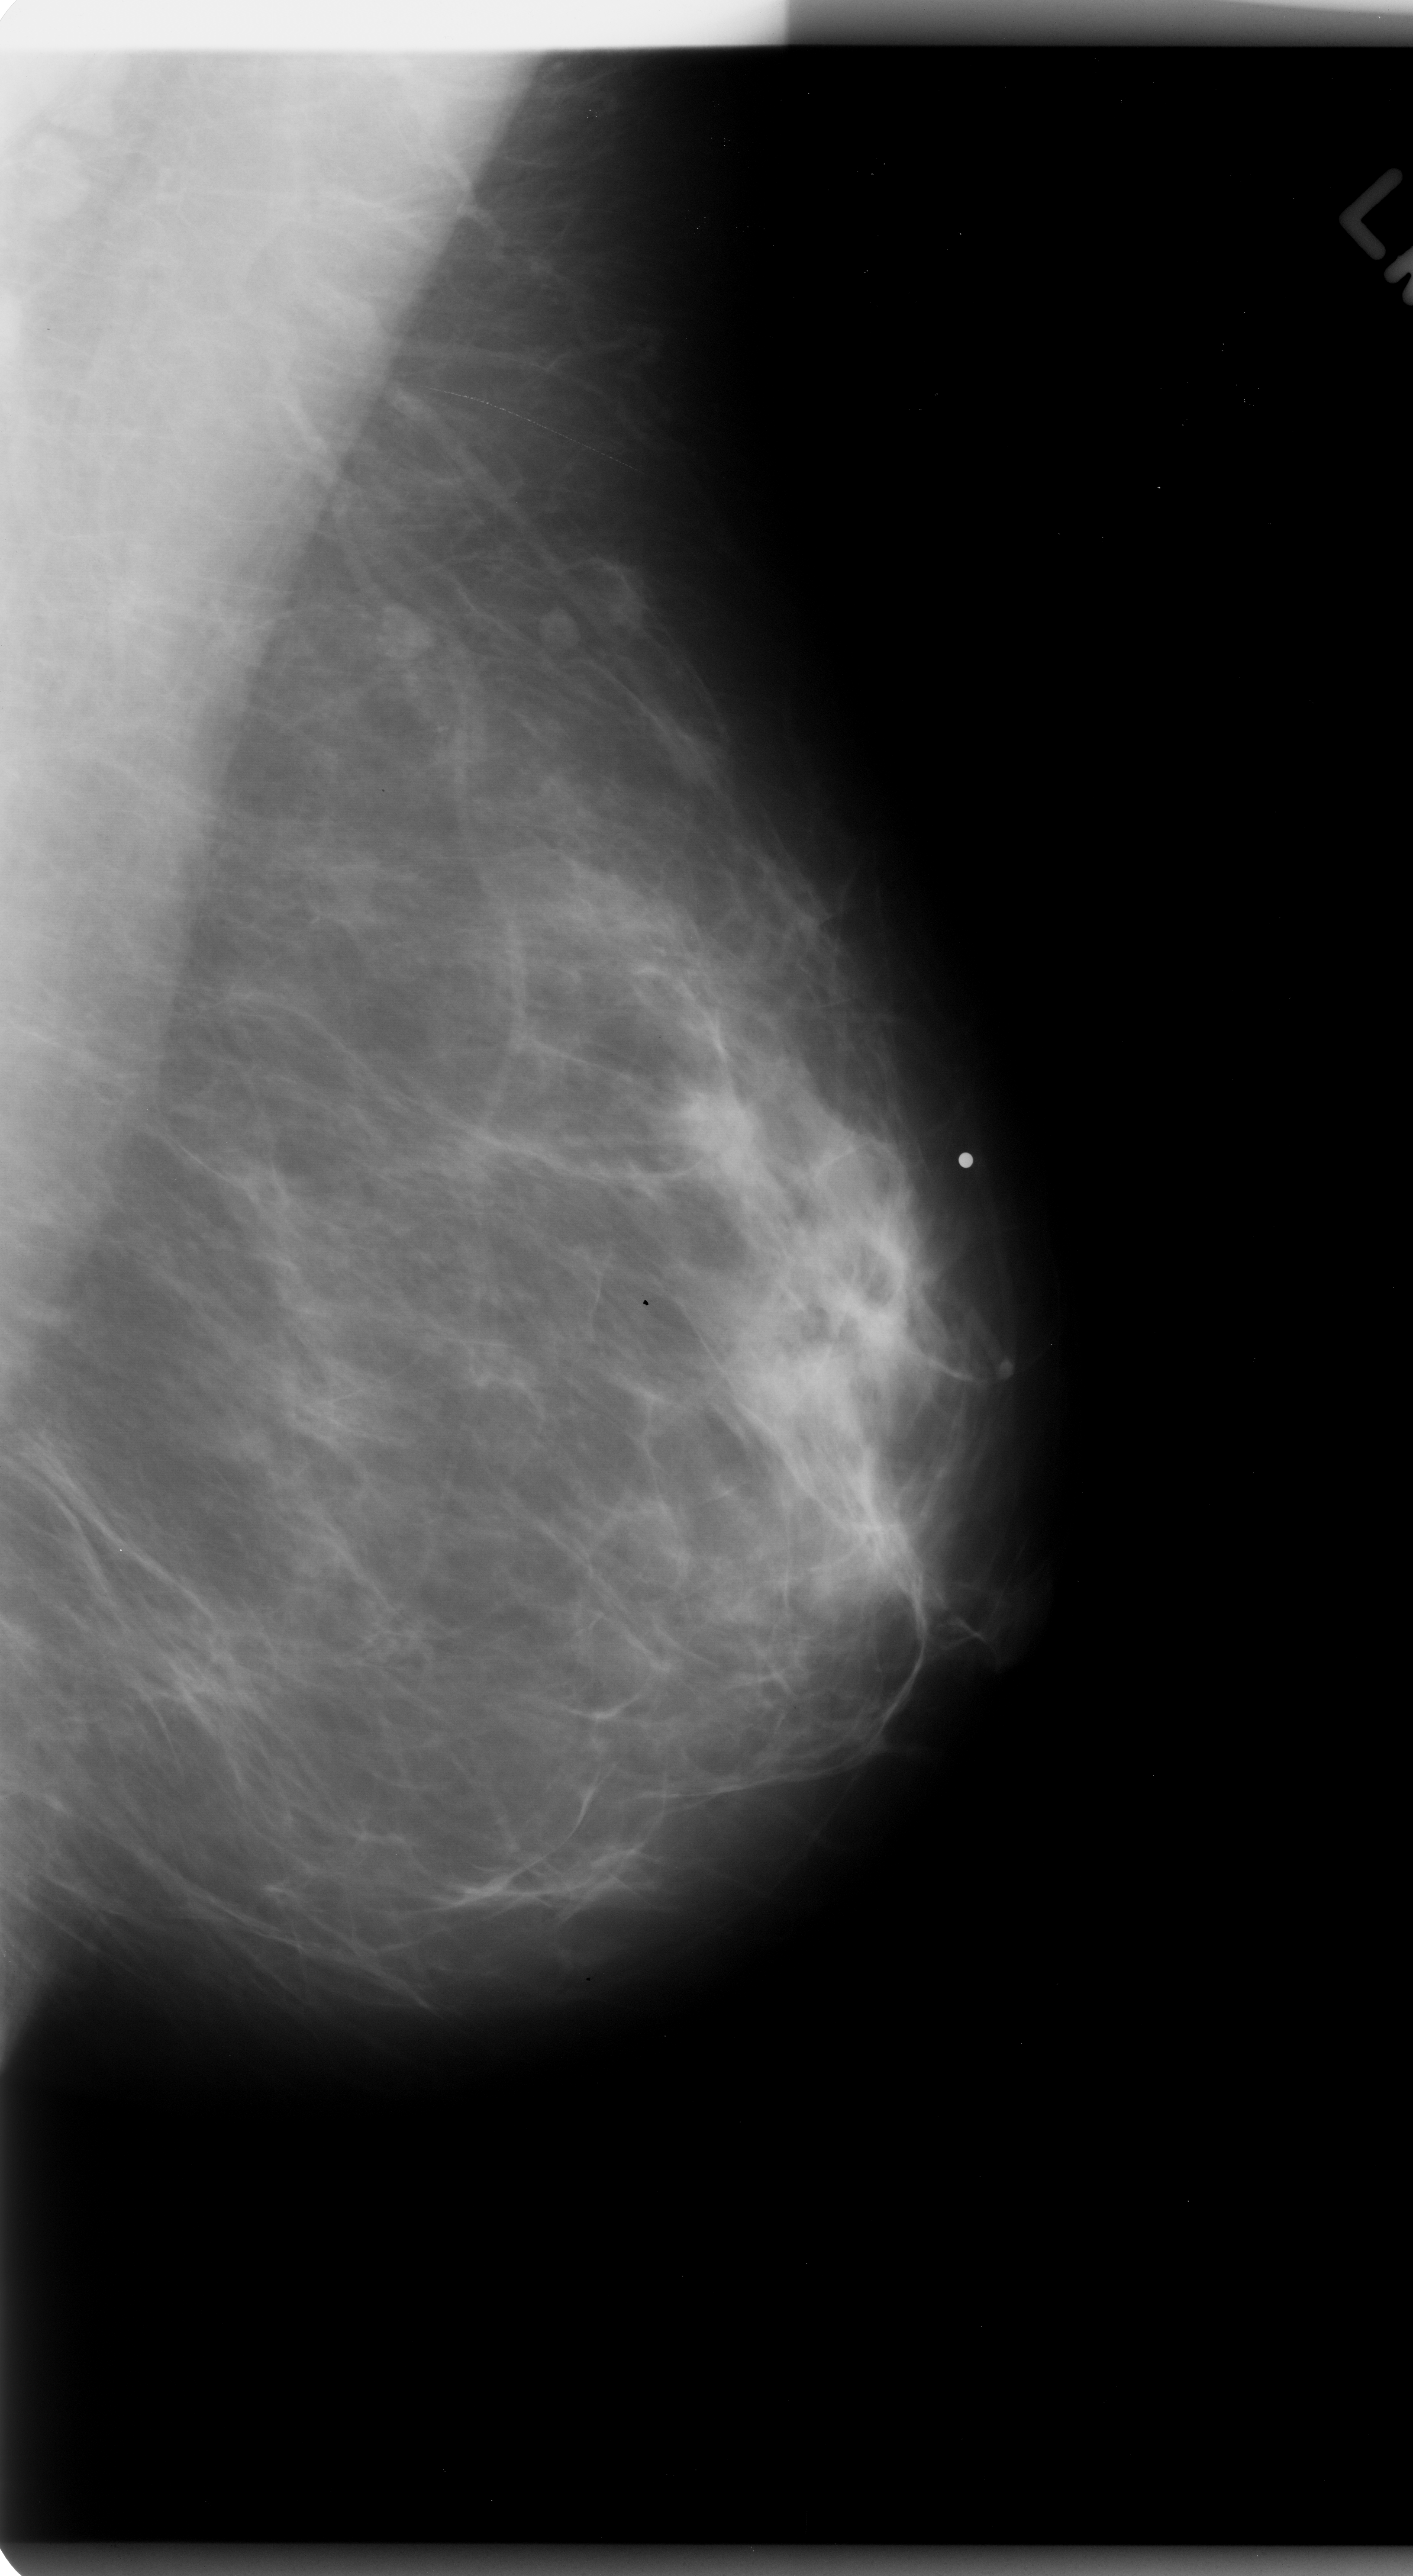
Digitized screen-film mammogram, left breast, MLO view, breast composition: scattered fibroglandular densities (BI-RADS density category 2 of 4).
- Radiologist-marked abnormalities on this image: mass, shape oval, margins spiculated; BI-RADS assessment category 5; pathology (as recorded): malignant.